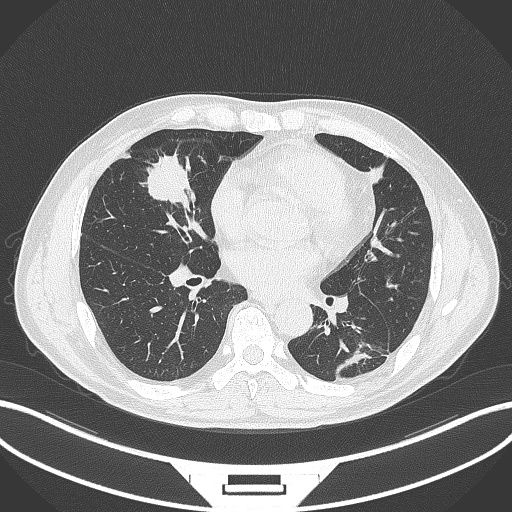
Chest CT, one axial slice; position 132 of 399 along the scan axis; reconstruction kernel B70f; 120 kVp; lung window (W 1500 / L -600 HU); 512 × 512 image matrix, field of view 400 × 400 mm. Patient: male, 59 years. Case-level facts recorded for this patient, not image findings: clinical TNM (as recorded): T2a N1 M0.
Annotated regions visible in this slice (bounding box drawn by a radiologist):
- lung tumour (recorded histology: adenocarcinoma): bounding box <140,153,198,208> (left, top, right, bottom; pixels)